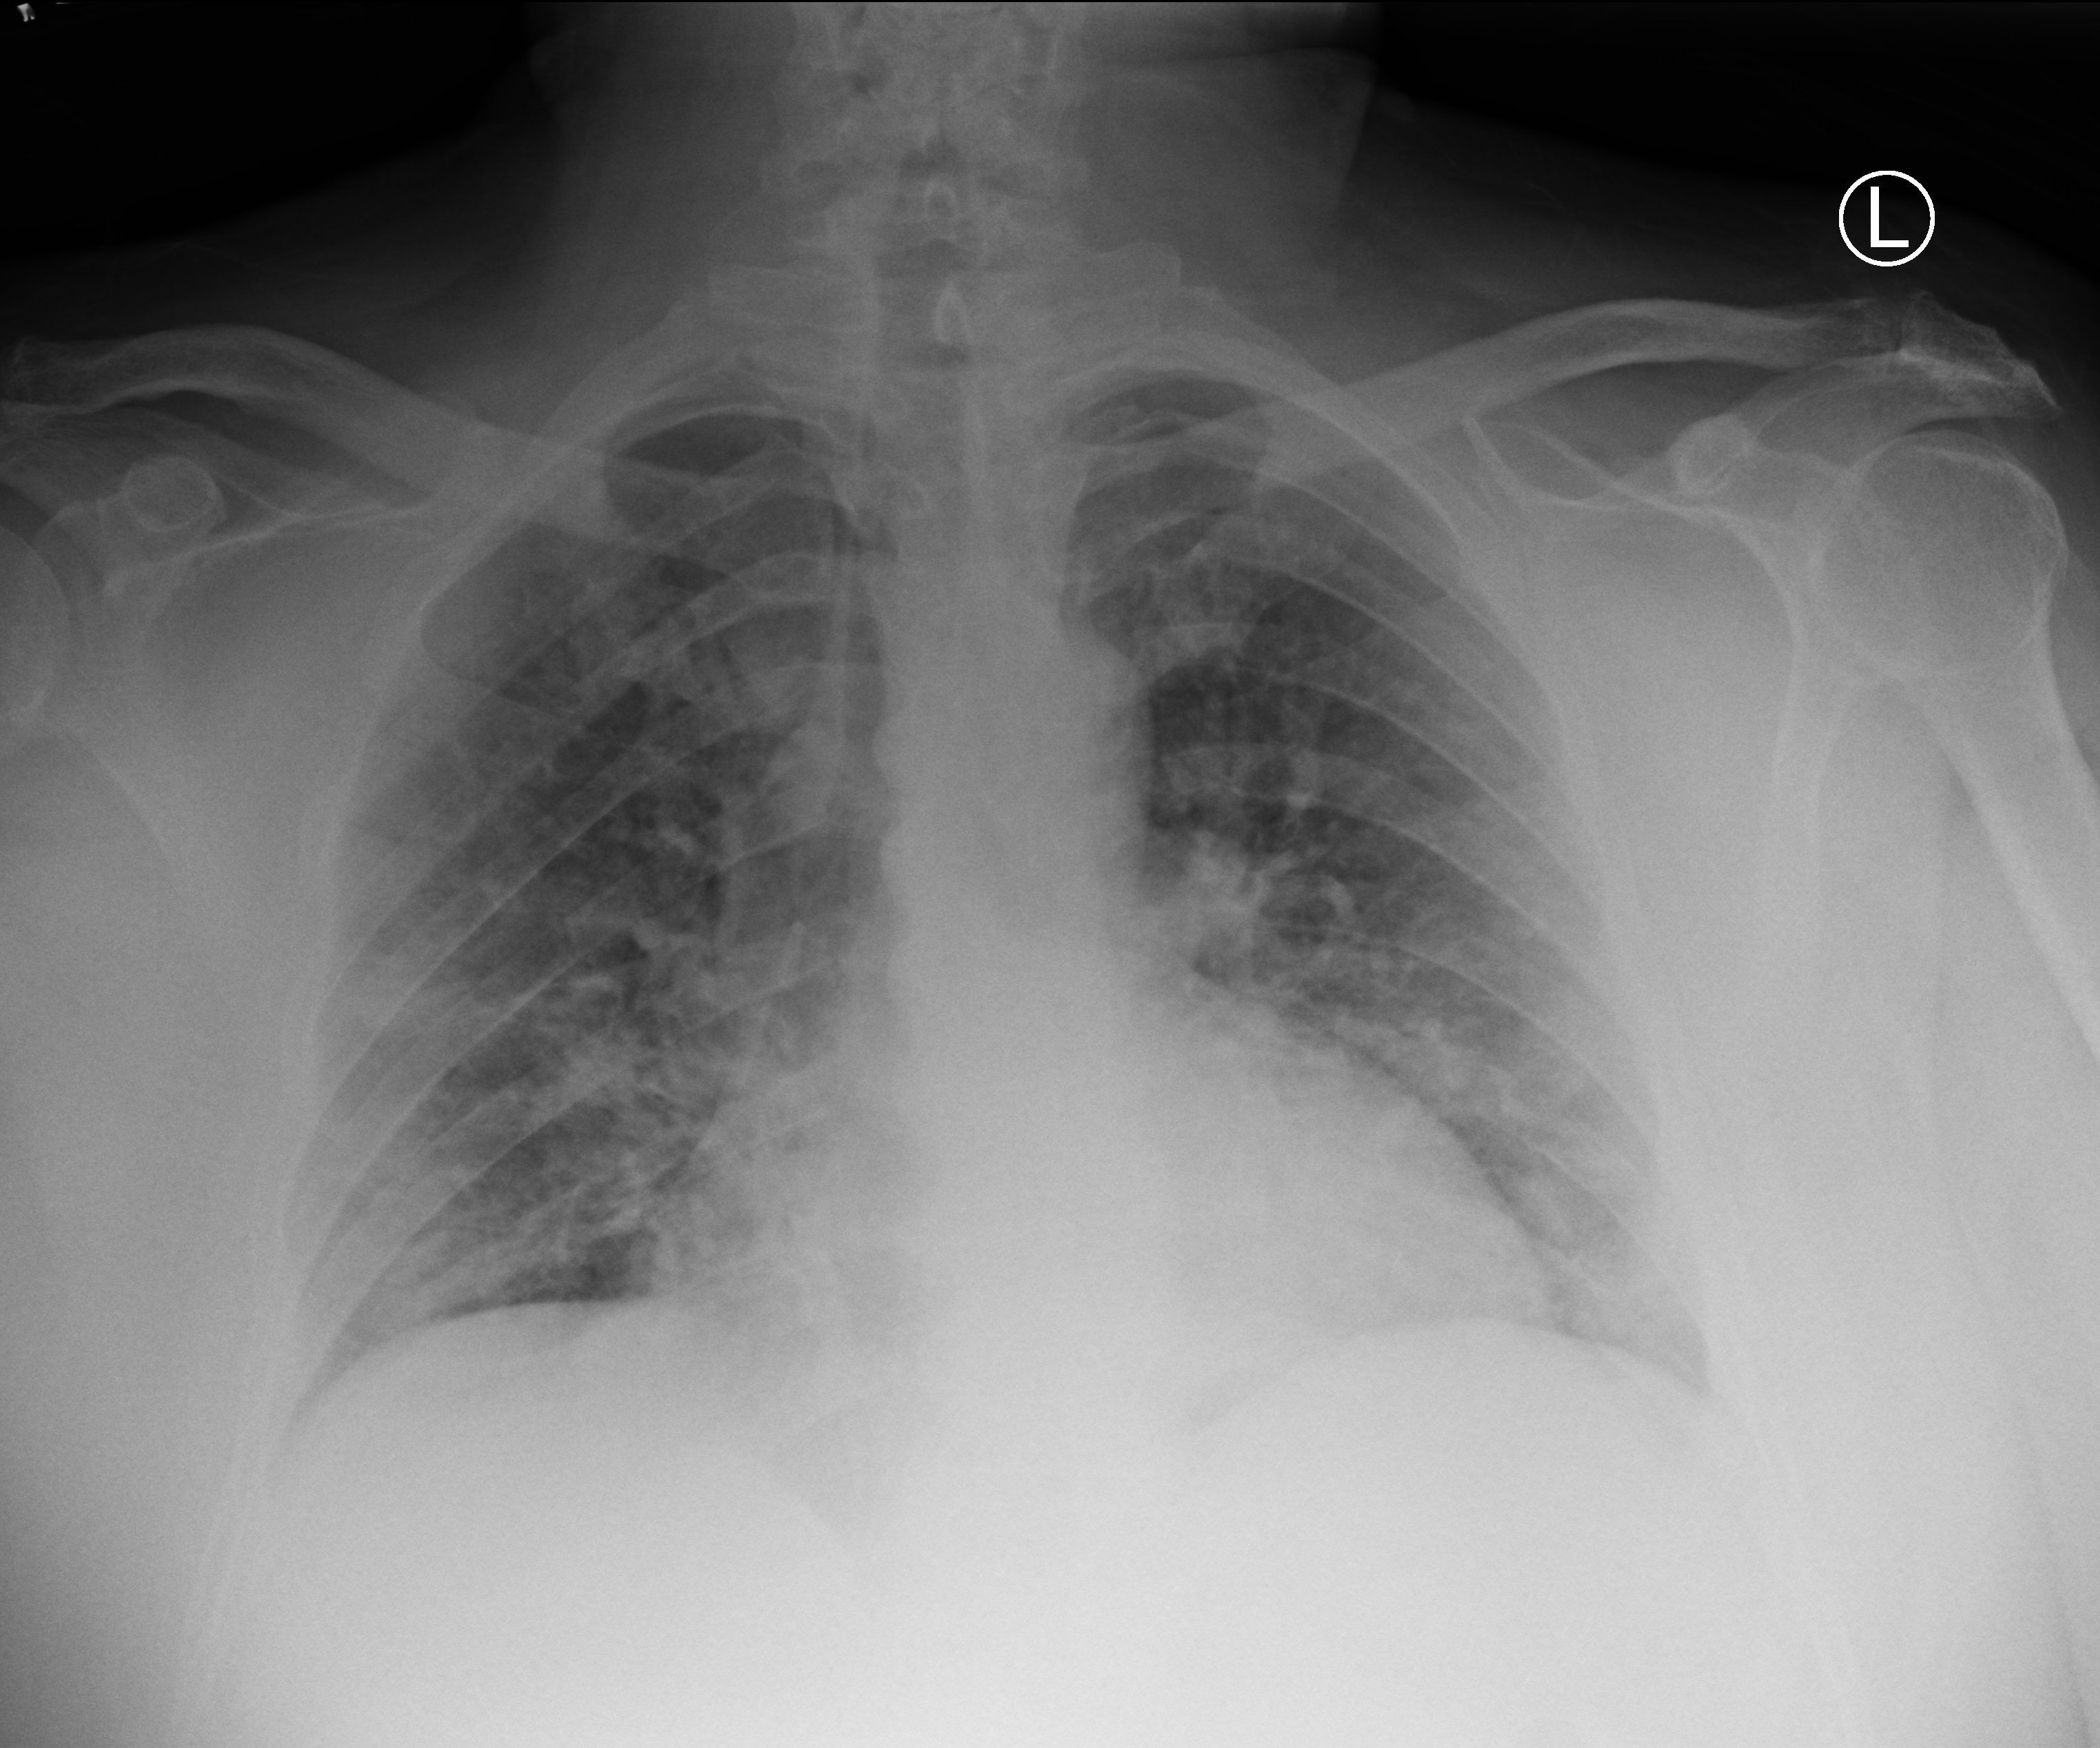
Portable chest radiograph, anteroposterior (AP) projection. Patient hospitalised with COVID-19; male, aged 18–59 years.
Admission-level facts for this patient (not findings on this image; timing relative to this image not recorded):
- mechanically ventilated during this hospital stay: no
- admitted to intensive care during this hospital stay: no
- chronic kidney disease (admission record): no